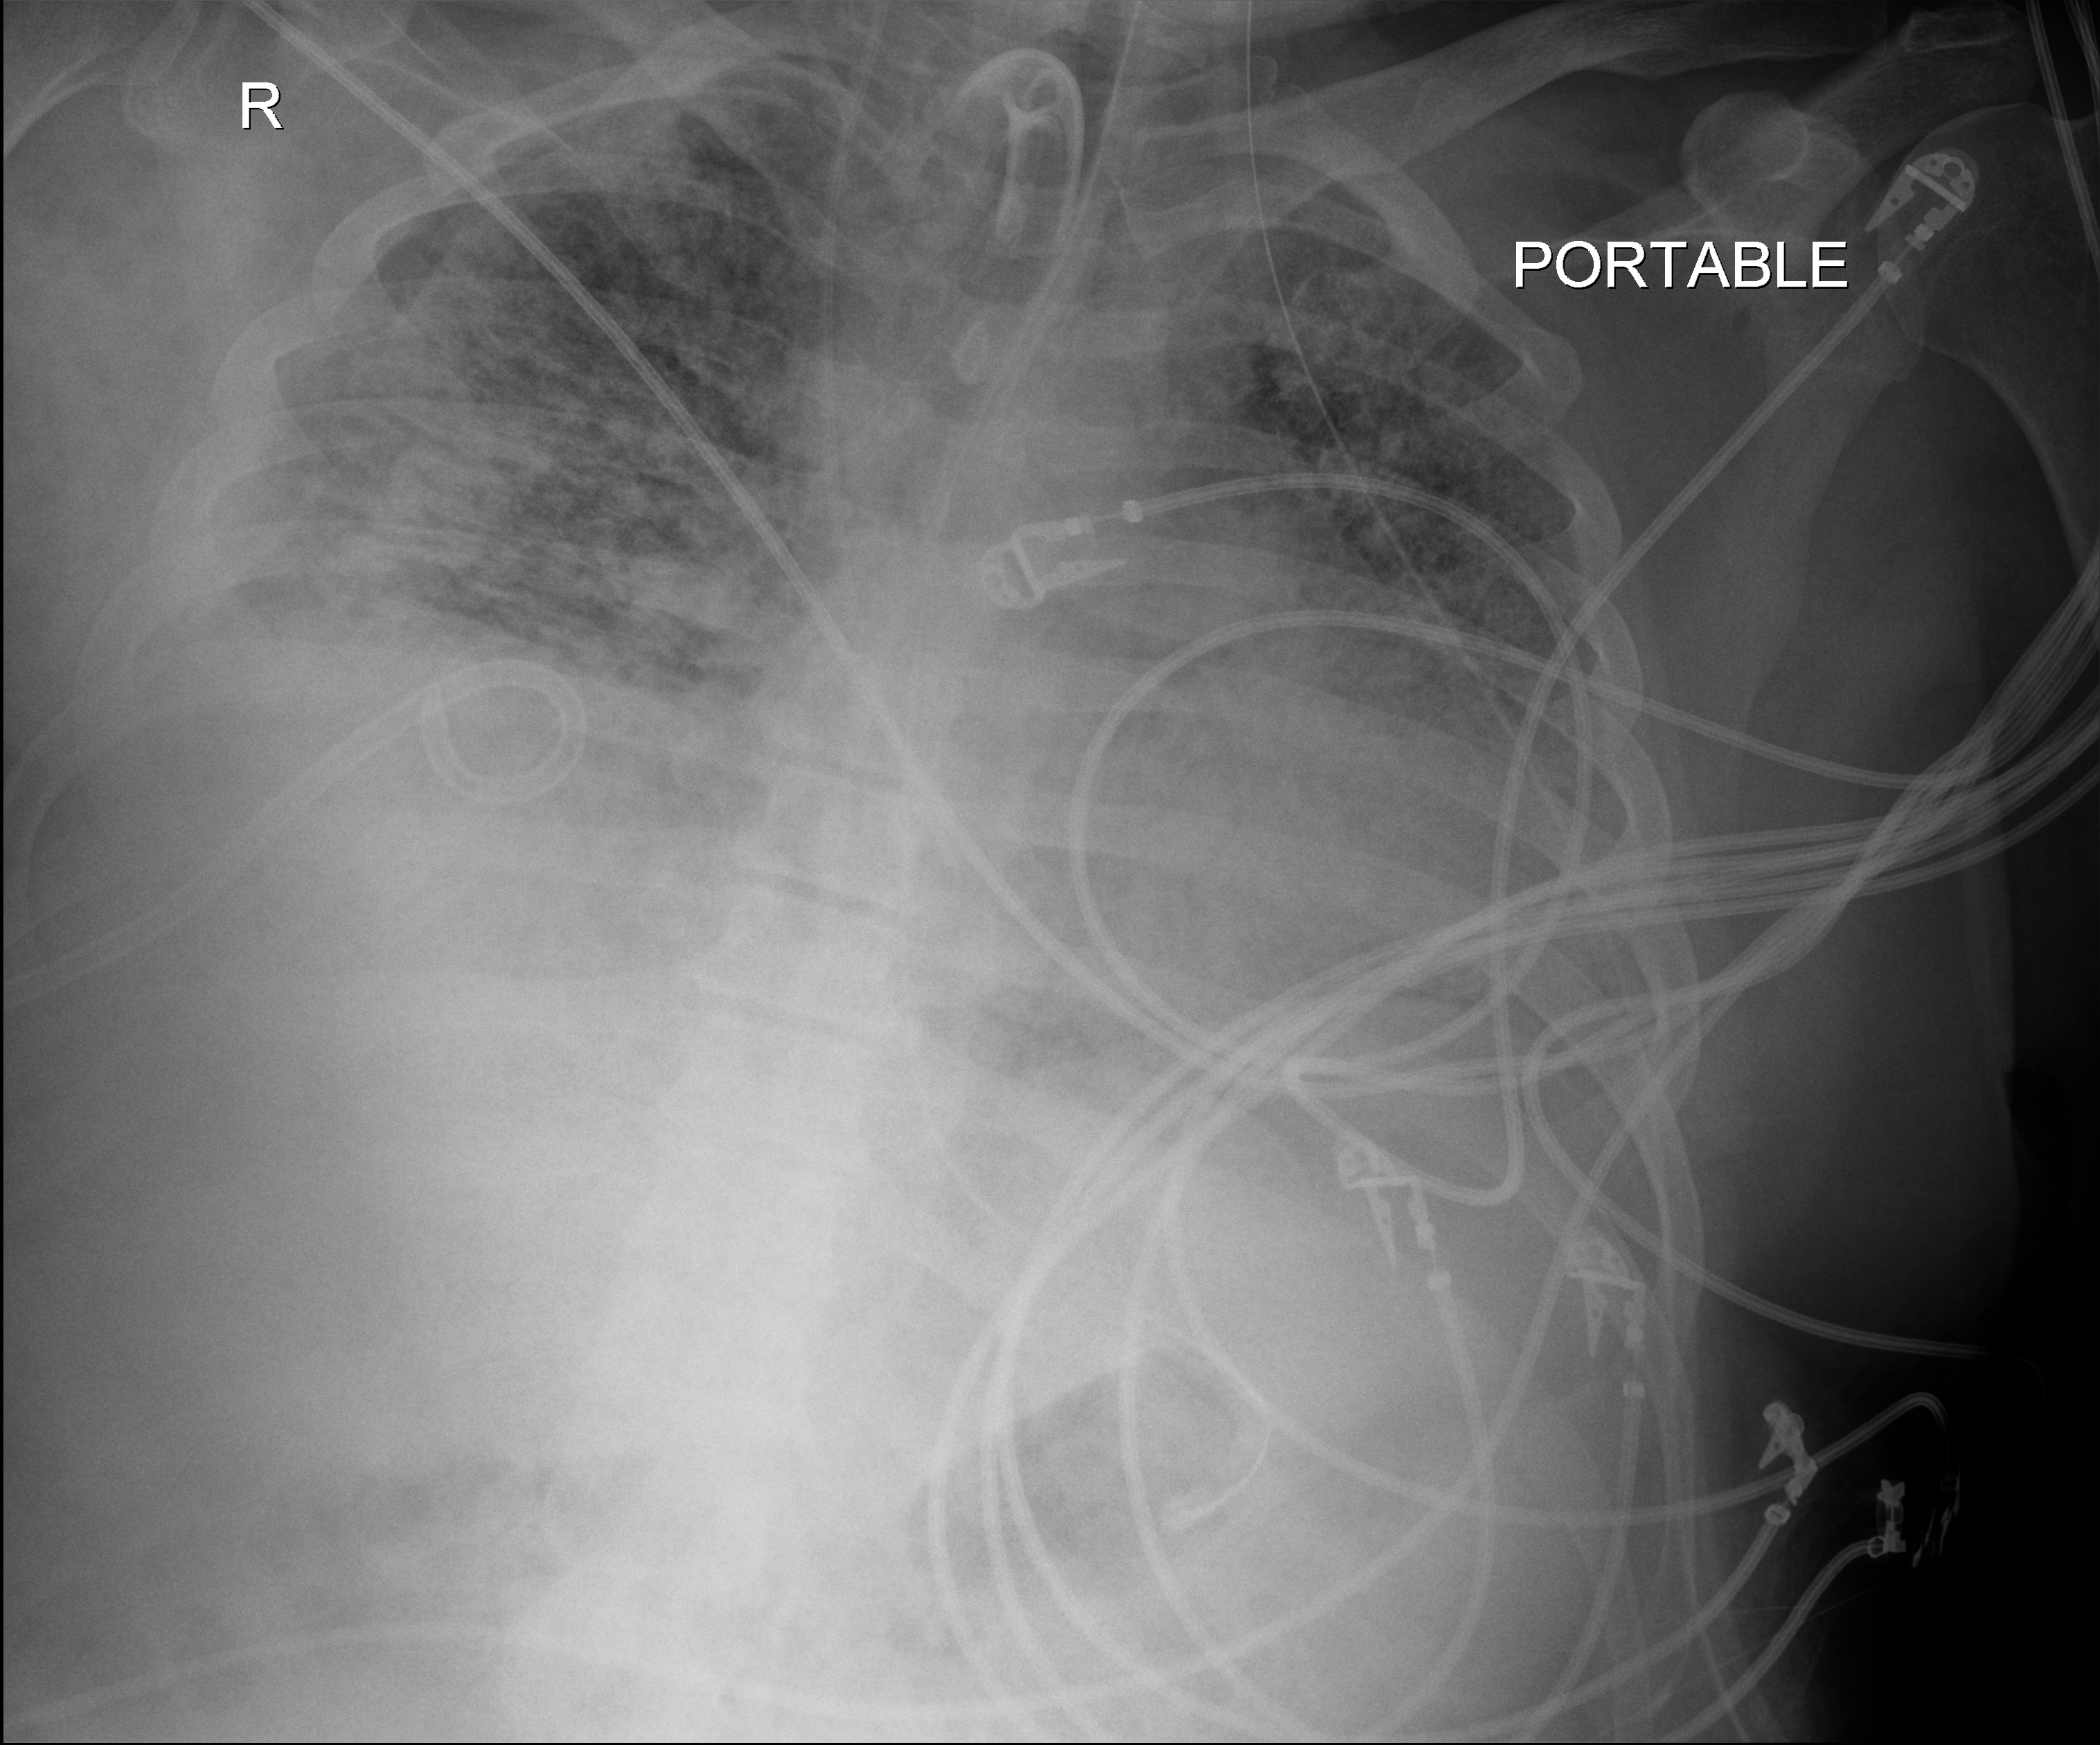
Bedside chest radiograph (digital radiography), anteroposterior (AP) projection. Male patient hospitalised with COVID-19, age 18–59 years.
From the hospital-stay record, not from the radiograph (when in the stay this image was taken is not recorded):
- admitted to intensive care during this hospital stay: yes